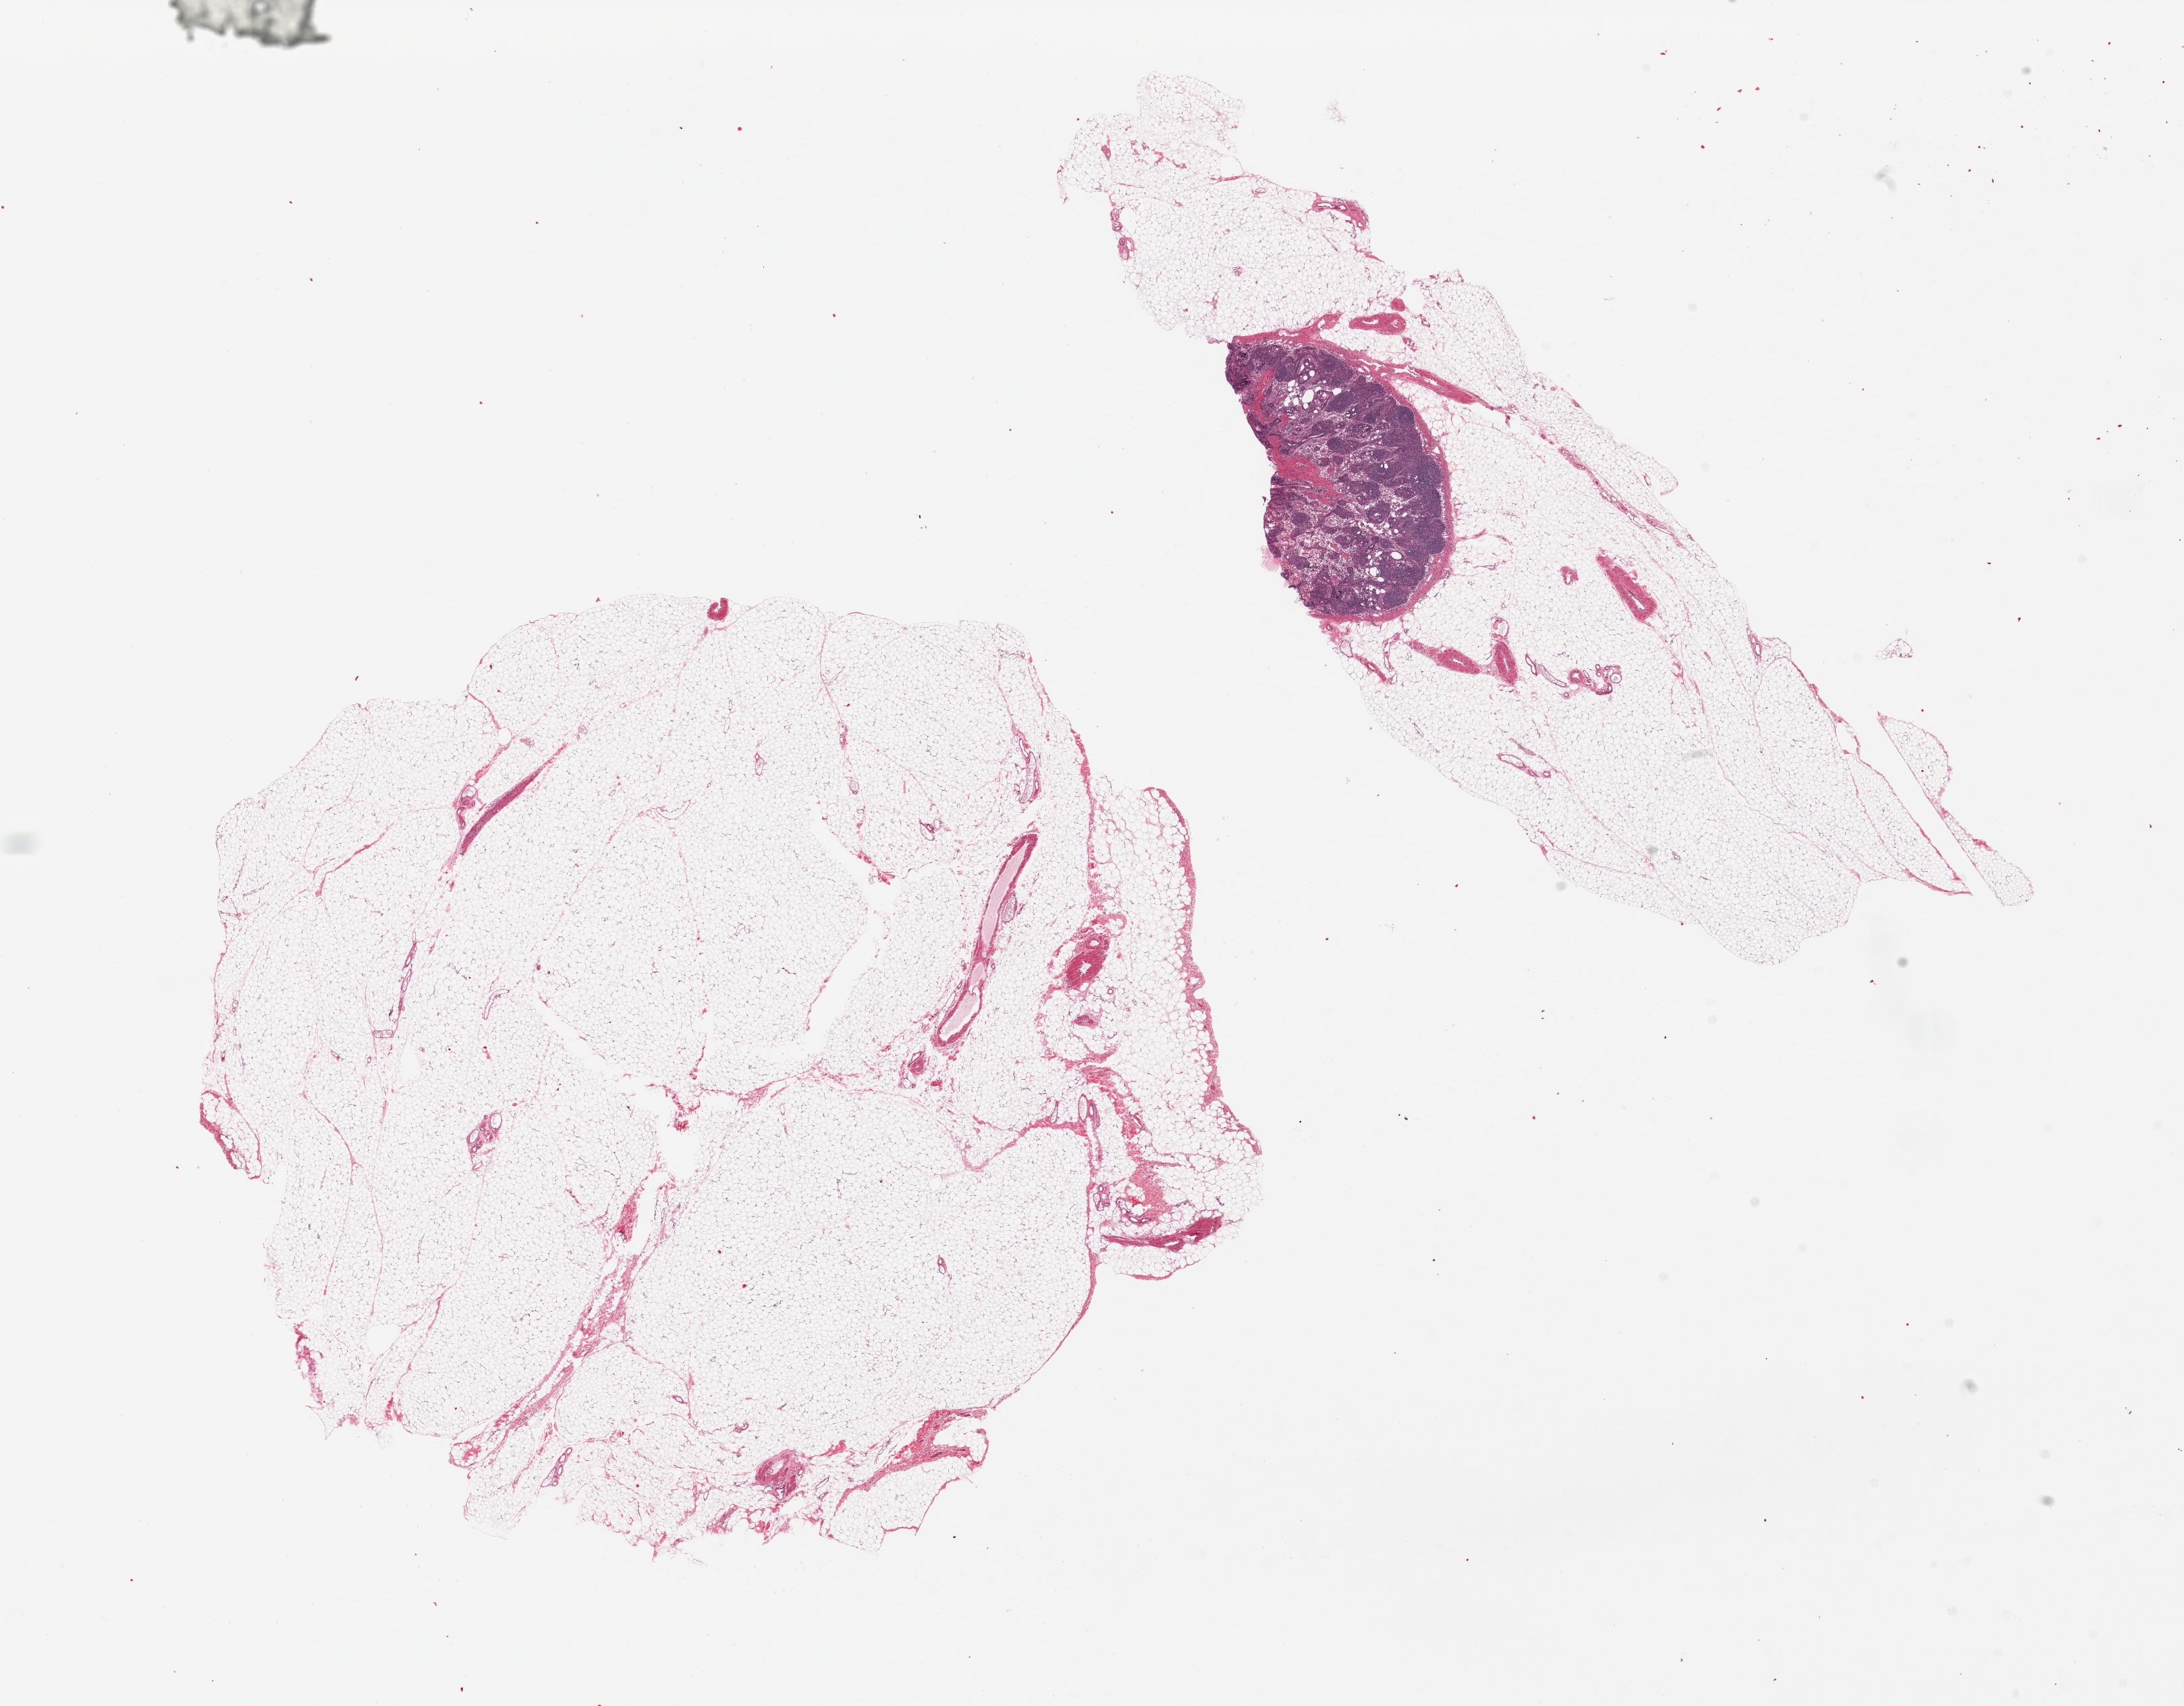
Haematoxylin and eosin whole-slide image — whole scanned area (about 25.6 x 20.0 mm, acquisition: 20x scan) shown as a low-resolution overview, PAXgene-fixed paraffin-embedded (PFPE) section, target tissue: omentum, donor tissue sample. Donor: male.
Pathologist's review note for this sample: 2 pieces; Smaller piece has a 3x2mm lymph node.